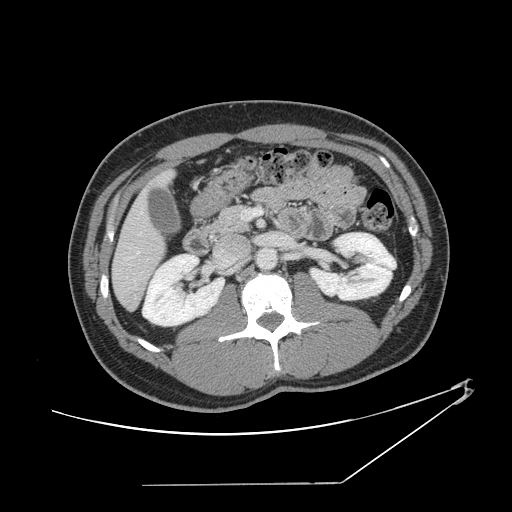
Contrast-enhanced abdominal CT, one axial slice. Reconstruction kernel STANDARD. Intravenous contrast given. Soft-tissue window (W 400 / L 40 HU). 512 × 512 image matrix, field of view 432 × 432 mm. Male patient, age 45 years. Case-level facts recorded for this patient, not image findings: diagnosis: colorectal cancer liver metastases, imaged before liver resection; multiple liver metastases: no; largest metastasis: 1 cm.
Outlined on this slice (manually delineated by an expert):
- hepatic veins: box from (x=124, y=250) to (x=140, y=260) px
- liver: (x=114, y=195)–(x=165, y=309)
- planned liver remnant (the part of the liver to remain after resection): (x=114, y=195)–(x=165, y=309)
- portal vein (with intrahepatic branches): (x=242, y=209)–(x=263, y=219)